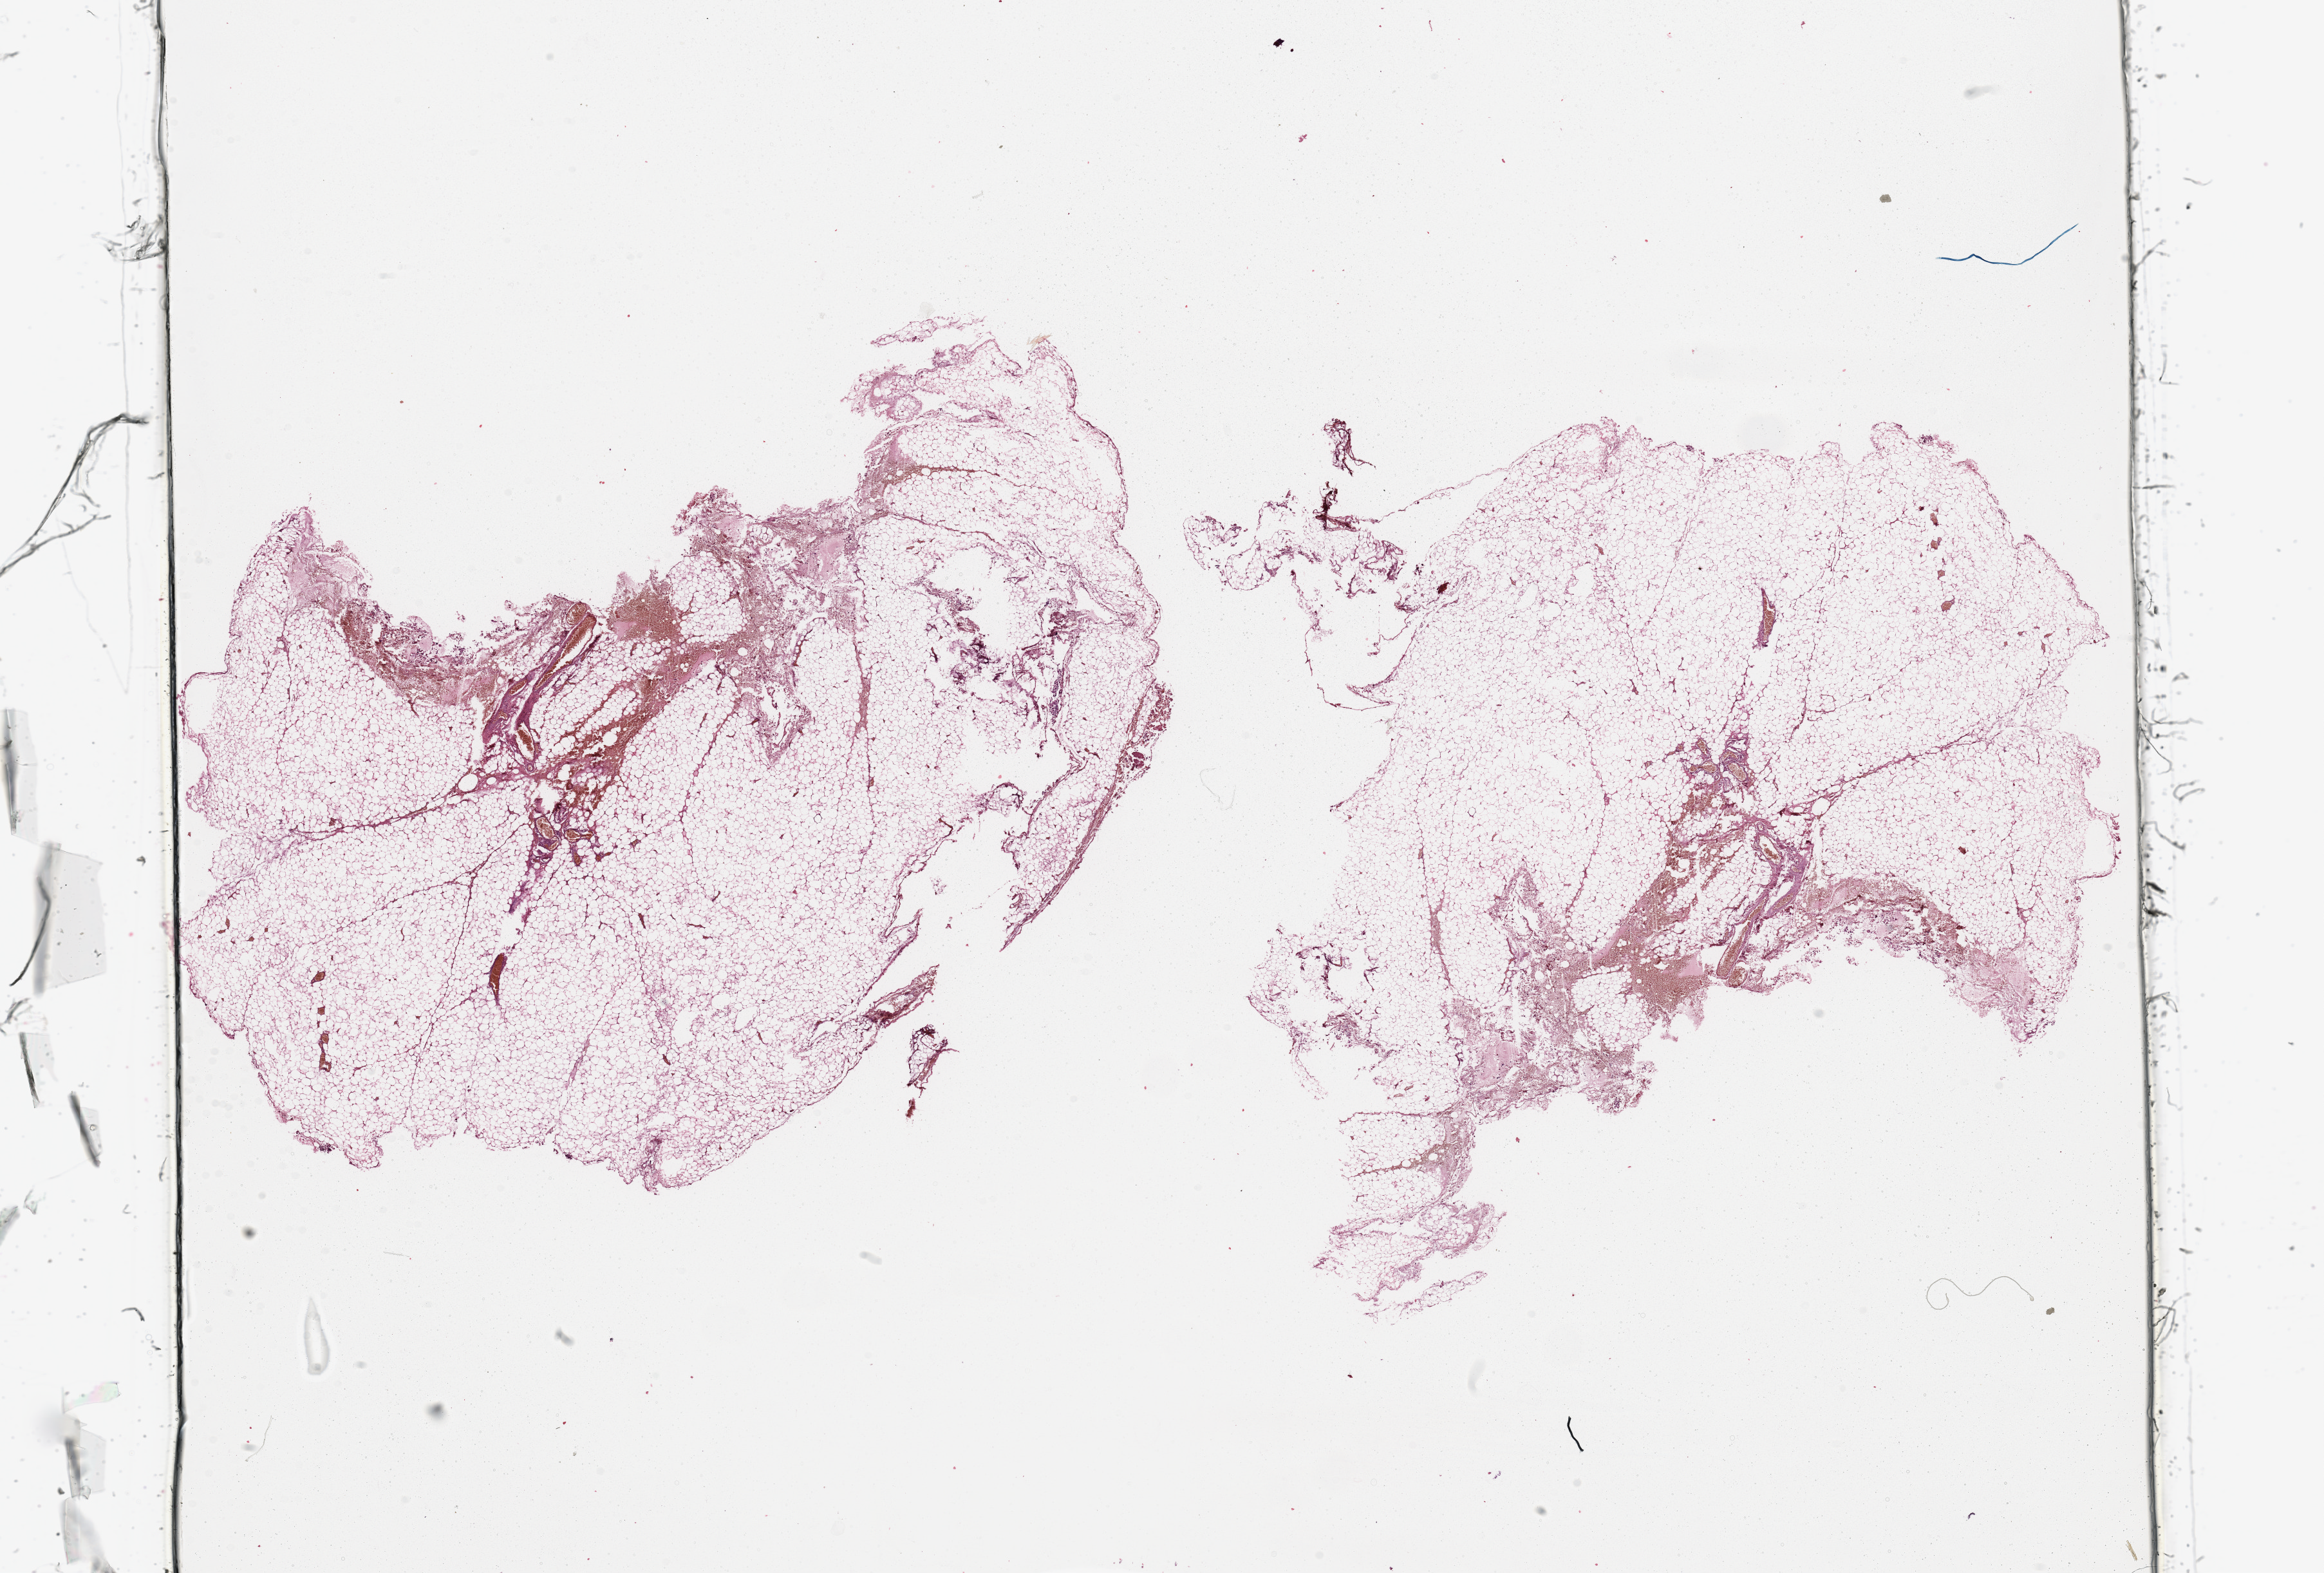
Digitized H&E tissue section (whole slide), a low-resolution overview of the entire scanned area, about 28.5 x 19.3 mm, normal (non-tumour) tissue (melanoma cohort); sampled site not recorded. Male, 33 y/o.
This section: normal (non-tumour) tissue from the same patient. Patient diagnosis: Malignant melanoma, NOS.